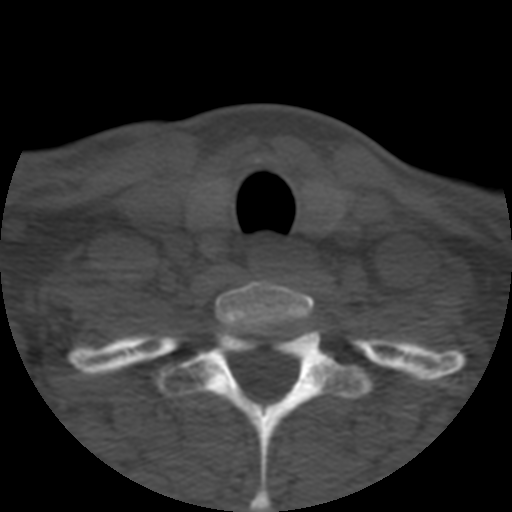
CT including the spine, one axial slice. Position 453 of 508 along the scan axis. Reconstruction kernel STANDARD. 120 kVp. Bone window (W 1800 / L 400 HU). 512 × 512 image matrix. Patient age 57 years. From the clinical record (not read from this slice): primary cancer: prostate.
Outlined on this slice (semi-automatically segmented with operator editing):
- T1 vertebra: bounding box [x1, y1, x2, y2] px = [93, 331, 412, 512]